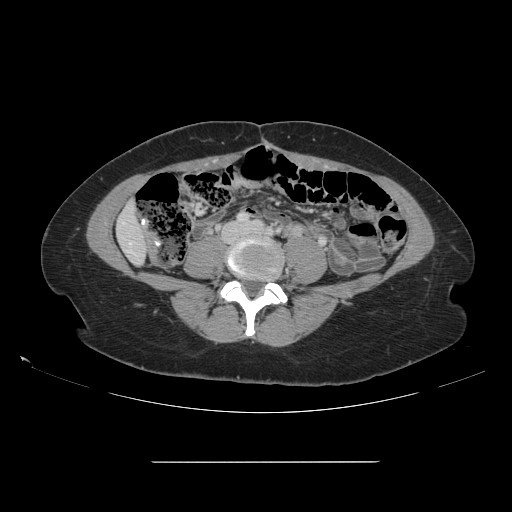
Contrast-enhanced abdominal CT, one axial slice; slice 15 of 151 in the series (ordered by position); 120 kVp; intravenous contrast given; soft-tissue window (W 400 / L 40 HU); 2.5 mm slice thickness; 512 × 512 image matrix, field of view 421 × 421 mm. Female patient, age 46 years. Case-level facts recorded for this patient, not image findings: diagnosis: colorectal cancer liver metastases, imaged before liver resection.
Outlined on this slice (expert manual segmentation):
- liver: box from (x=118, y=204) to (x=147, y=264) px
- planned liver remnant (the part of the liver to remain after resection): (x=118, y=204)–(x=148, y=264)